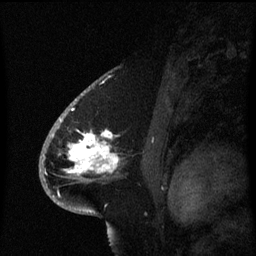
Breast MRI (dynamic contrast-enhanced), one sagittal slice; slice 41 of 60 in the series (ordered by position); dynamic contrast-enhanced series, image 2 of 3 at this slice position (ordered by acquisition); 1.5 T; TE 4.2 ms, TR 8.4 ms; 2.1 mm slice thickness; 256 × 256 image matrix, field of view 200 × 200 mm. Female patient, age 53 years. From the clinical record (not read from this slice): setting: breast cancer imaged before/during neoadjuvant chemotherapy; receptor status: HR-positive, HER2-negative.
Outlined on this slice (semi-automatic segmentation, software-assisted and operator-edited):
- analysis volume of interest (the breast-tissue region the enhancement analysis was run in; not a lesion): bounding box [x1, y1, x2, y2] px = [49, 108, 123, 201]
- tumour enhancement mask (voxels above the 70 % enhancement threshold inside the analysis volume of interest): [61, 120, 120, 175]